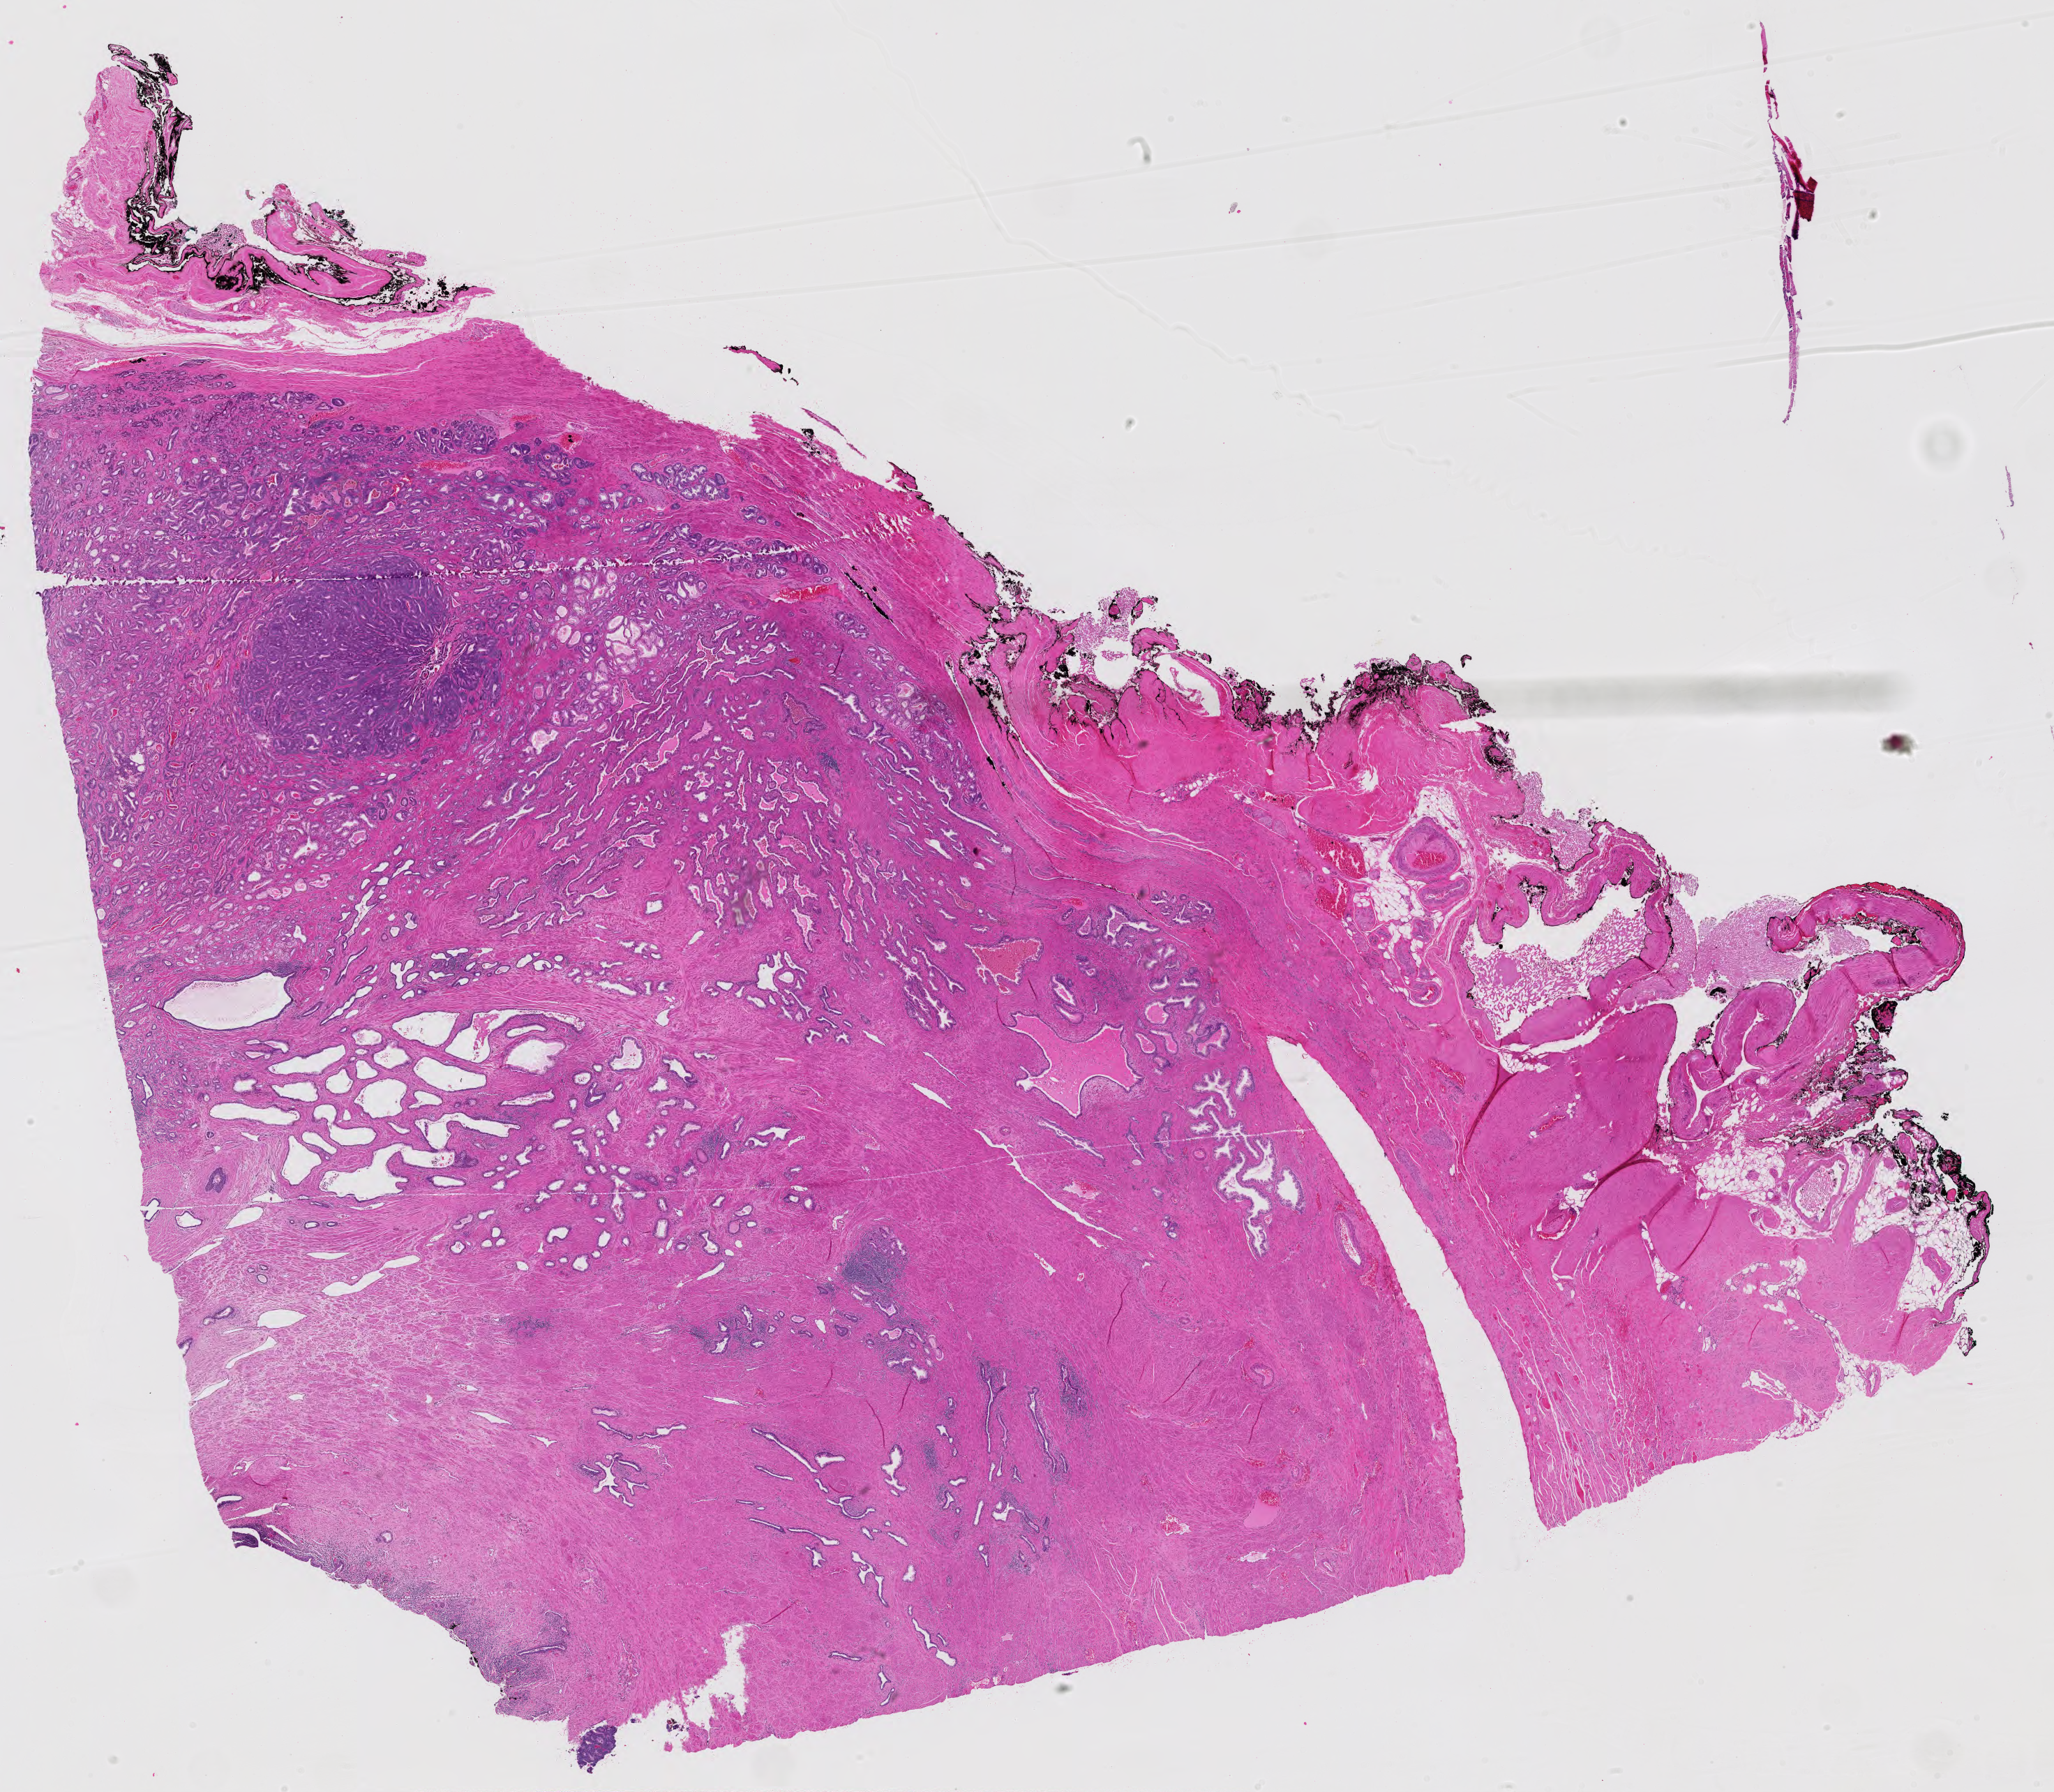
Whole-slide histology image, H&E — whole scanned area (about 21.4 x 18.6 mm, acquisition: 40x scan) shown as a low-resolution overview, formalin-fixed paraffin-embedded (FFPE) diagnostic section, sample: primary tumour, prostate. Male, age 74 years at initial diagnosis. Gleason score: 8 (4+4).
Pathologic diagnosis: Adenocarcinoma, NOS (prostate gland).